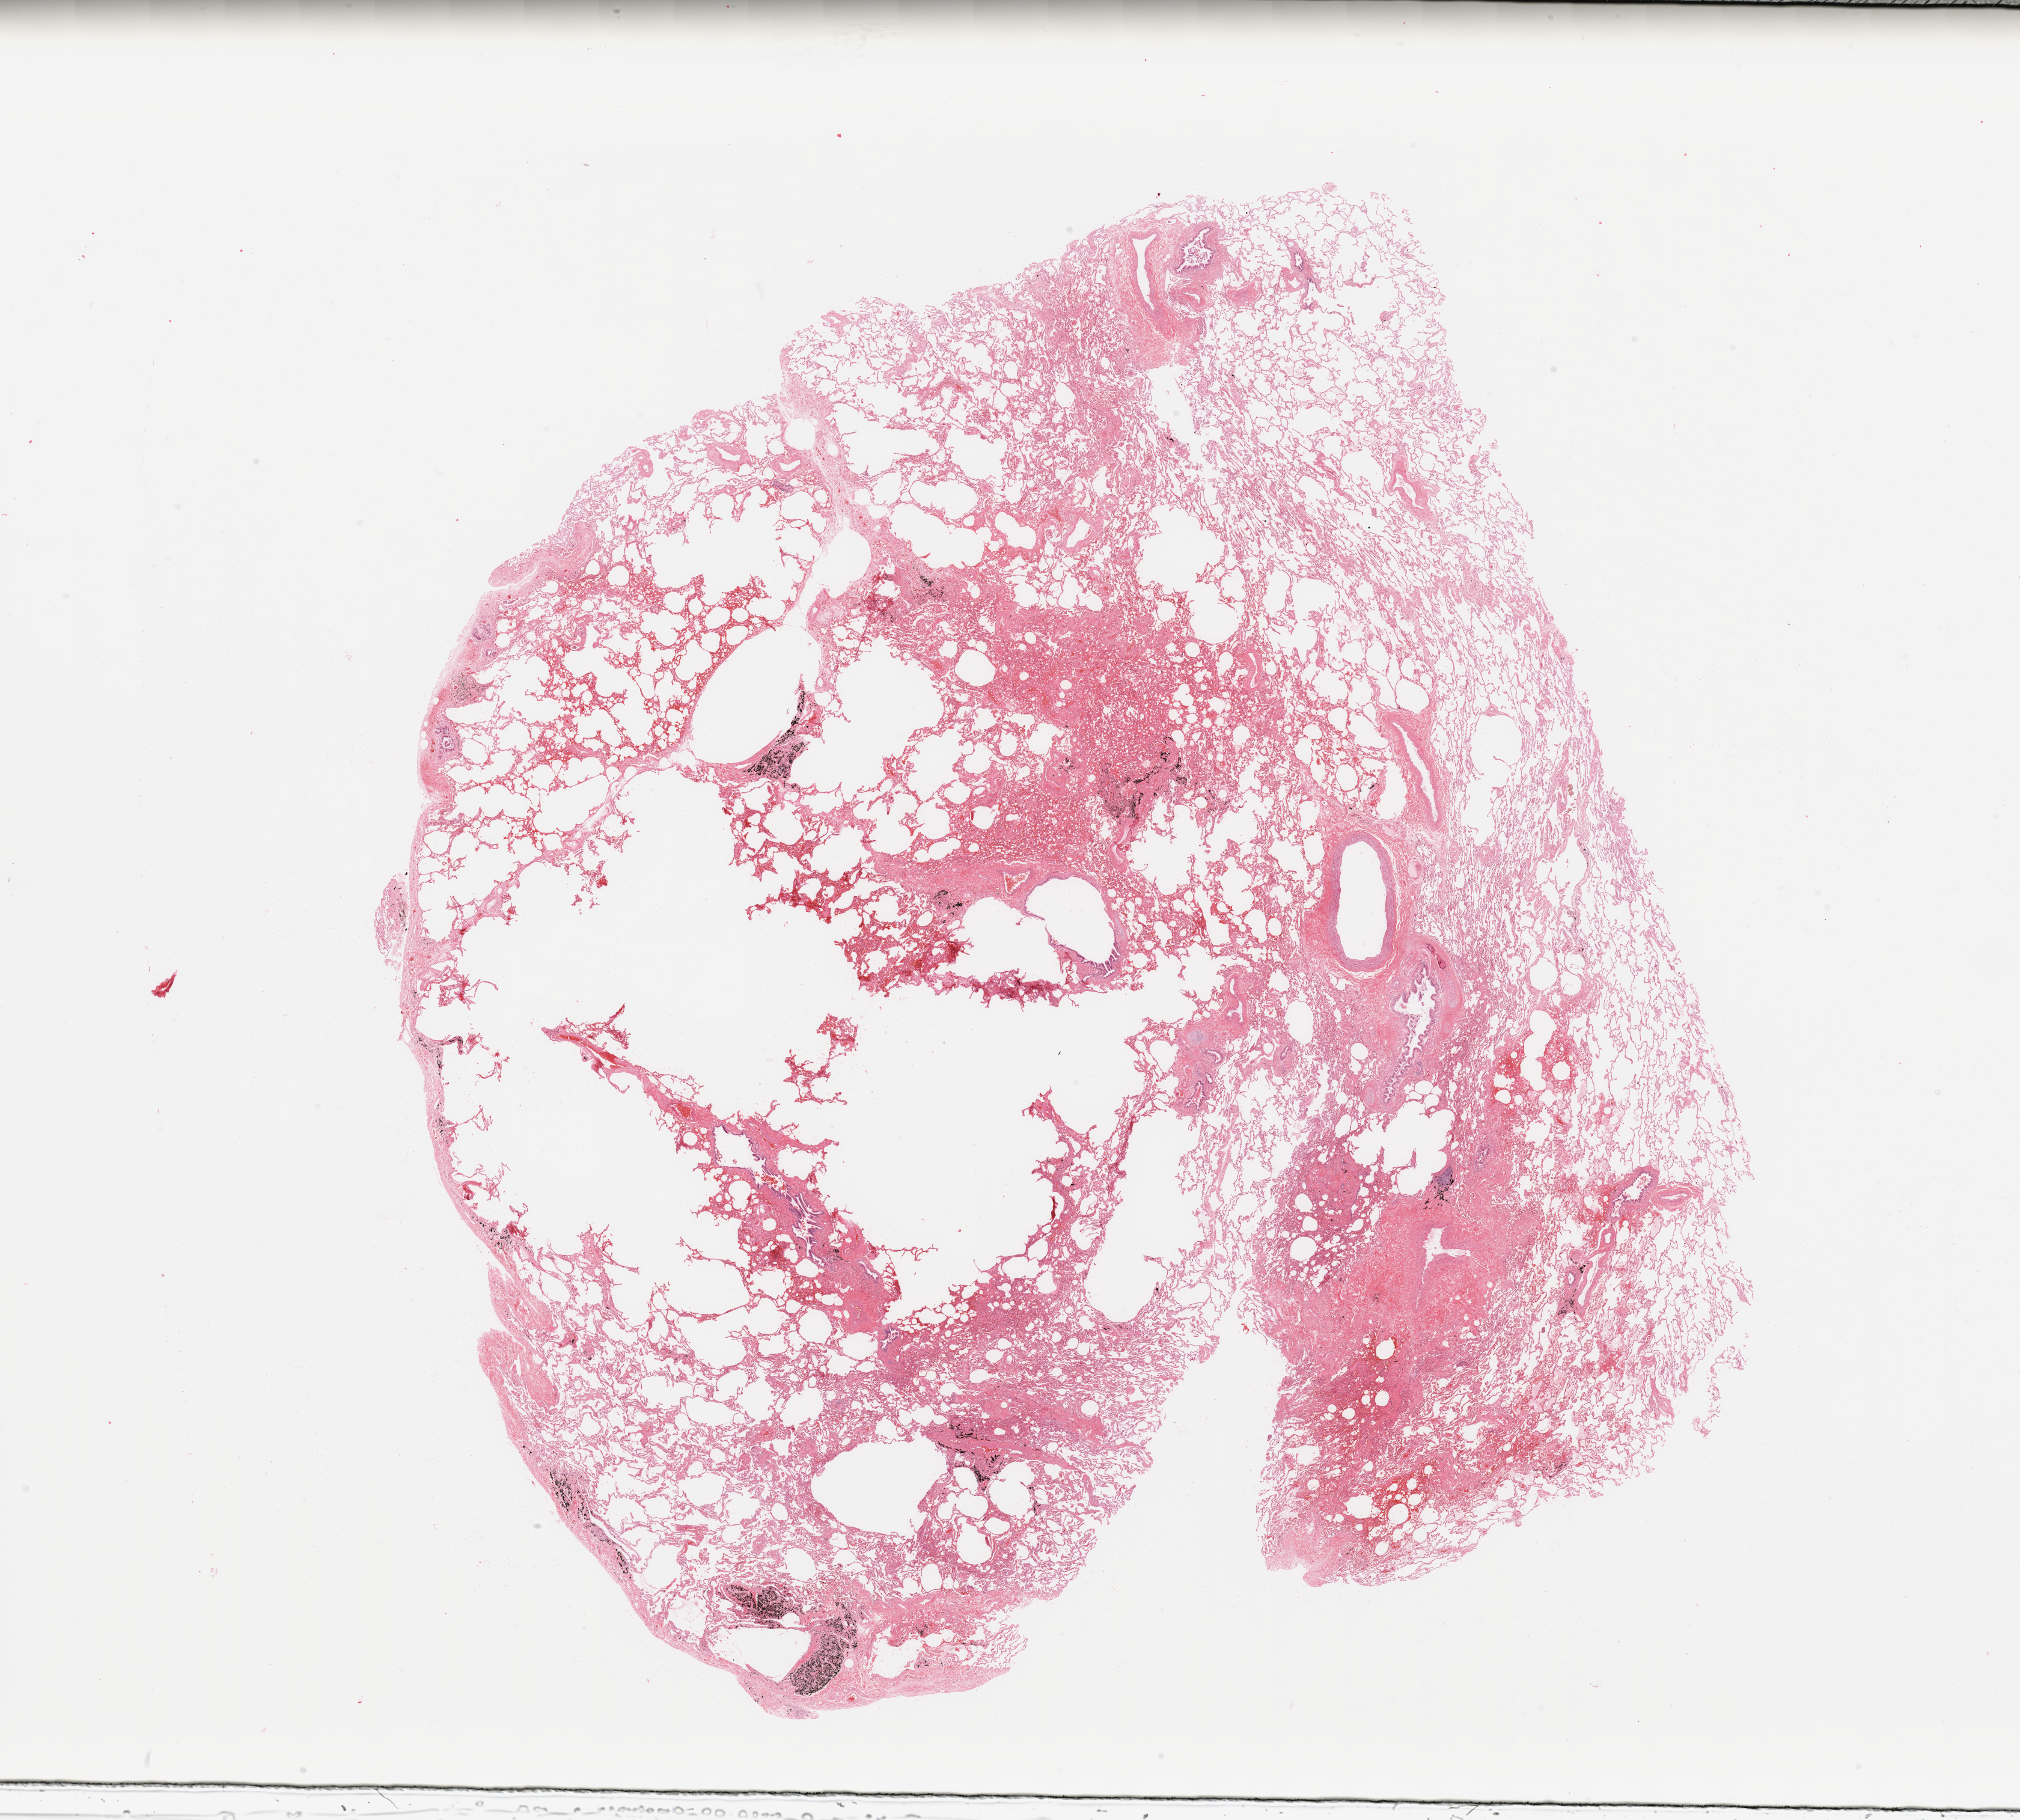
H&E whole-slide image — low-resolution overview of the scanned area, about 26.6 x 23.9 mm (slide scanned at 20x). Lung, normal (non-tumour) tissue. Patient: male, age 64 years.
• this section: normal (non-tumour) tissue from the same patient
• patient diagnosis: Adenocarcinoma, NOS